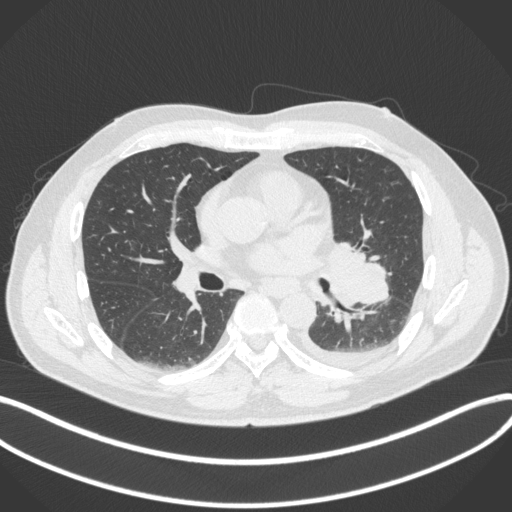
Chest CT, one axial slice. Slice 189 of 350 in the series (ordered by position). Reconstruction kernel B31f. Lung window (W 1500 / L -600 HU). 1 mm slice thickness. 512 × 512 image matrix, field of view 400 × 400 mm. Male patient, age 58 years. Case-level facts recorded for this patient, not image findings: clinical TNM (as recorded): T3 N1 M1b; histopathological grade: G3.
Annotated regions visible in this slice (rectangle marked by the reading radiologist):
- lung tumour (recorded histology: small cell carcinoma): box from (x=323, y=234) to (x=390, y=311) px